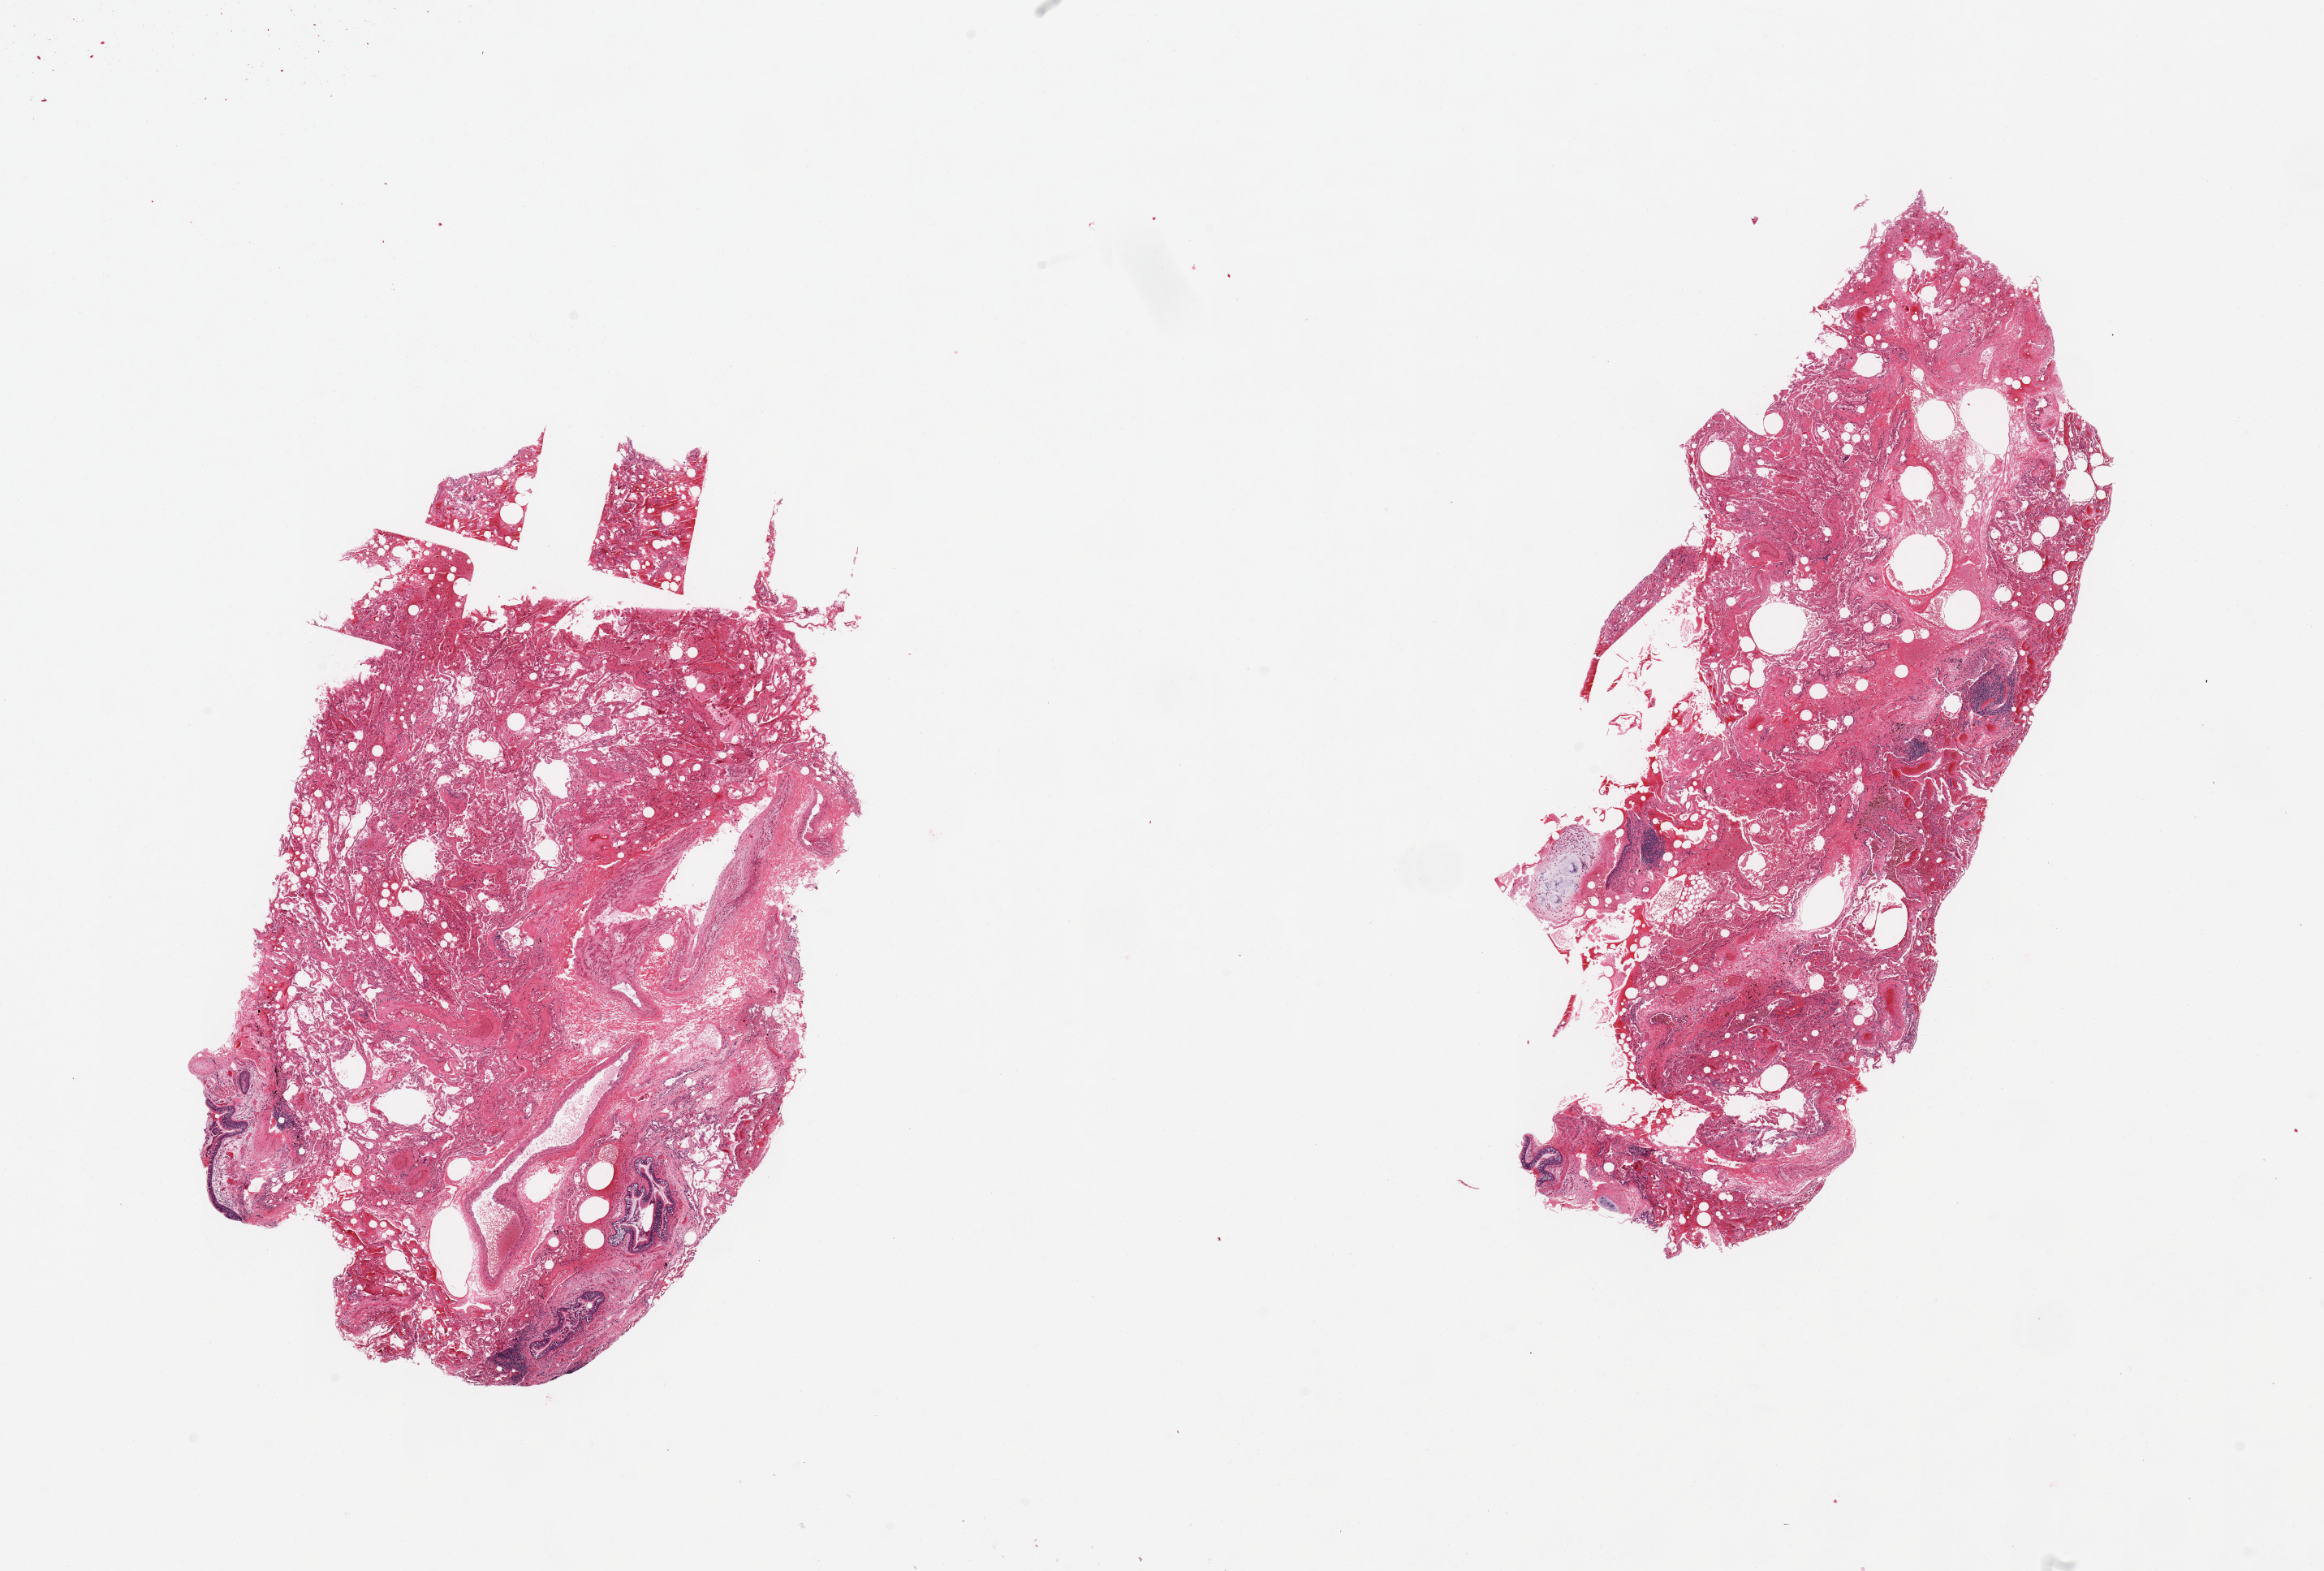
H&E whole-slide image, low-resolution overview of the scanned area, about 22.6 x 15.3 mm, PAXgene-fixed, paraffin-embedded tissue, section of lung (target tissue), tissue donor sample. Donor: male.
Reviewer comment on this tissue sample: 2 pieces; marked chronic passive congestion; emphysematous changes; bronchioles; small fragment of cartilage; a few scattered small lymphocytic aggregates; fragment of bronchiole and mucous.